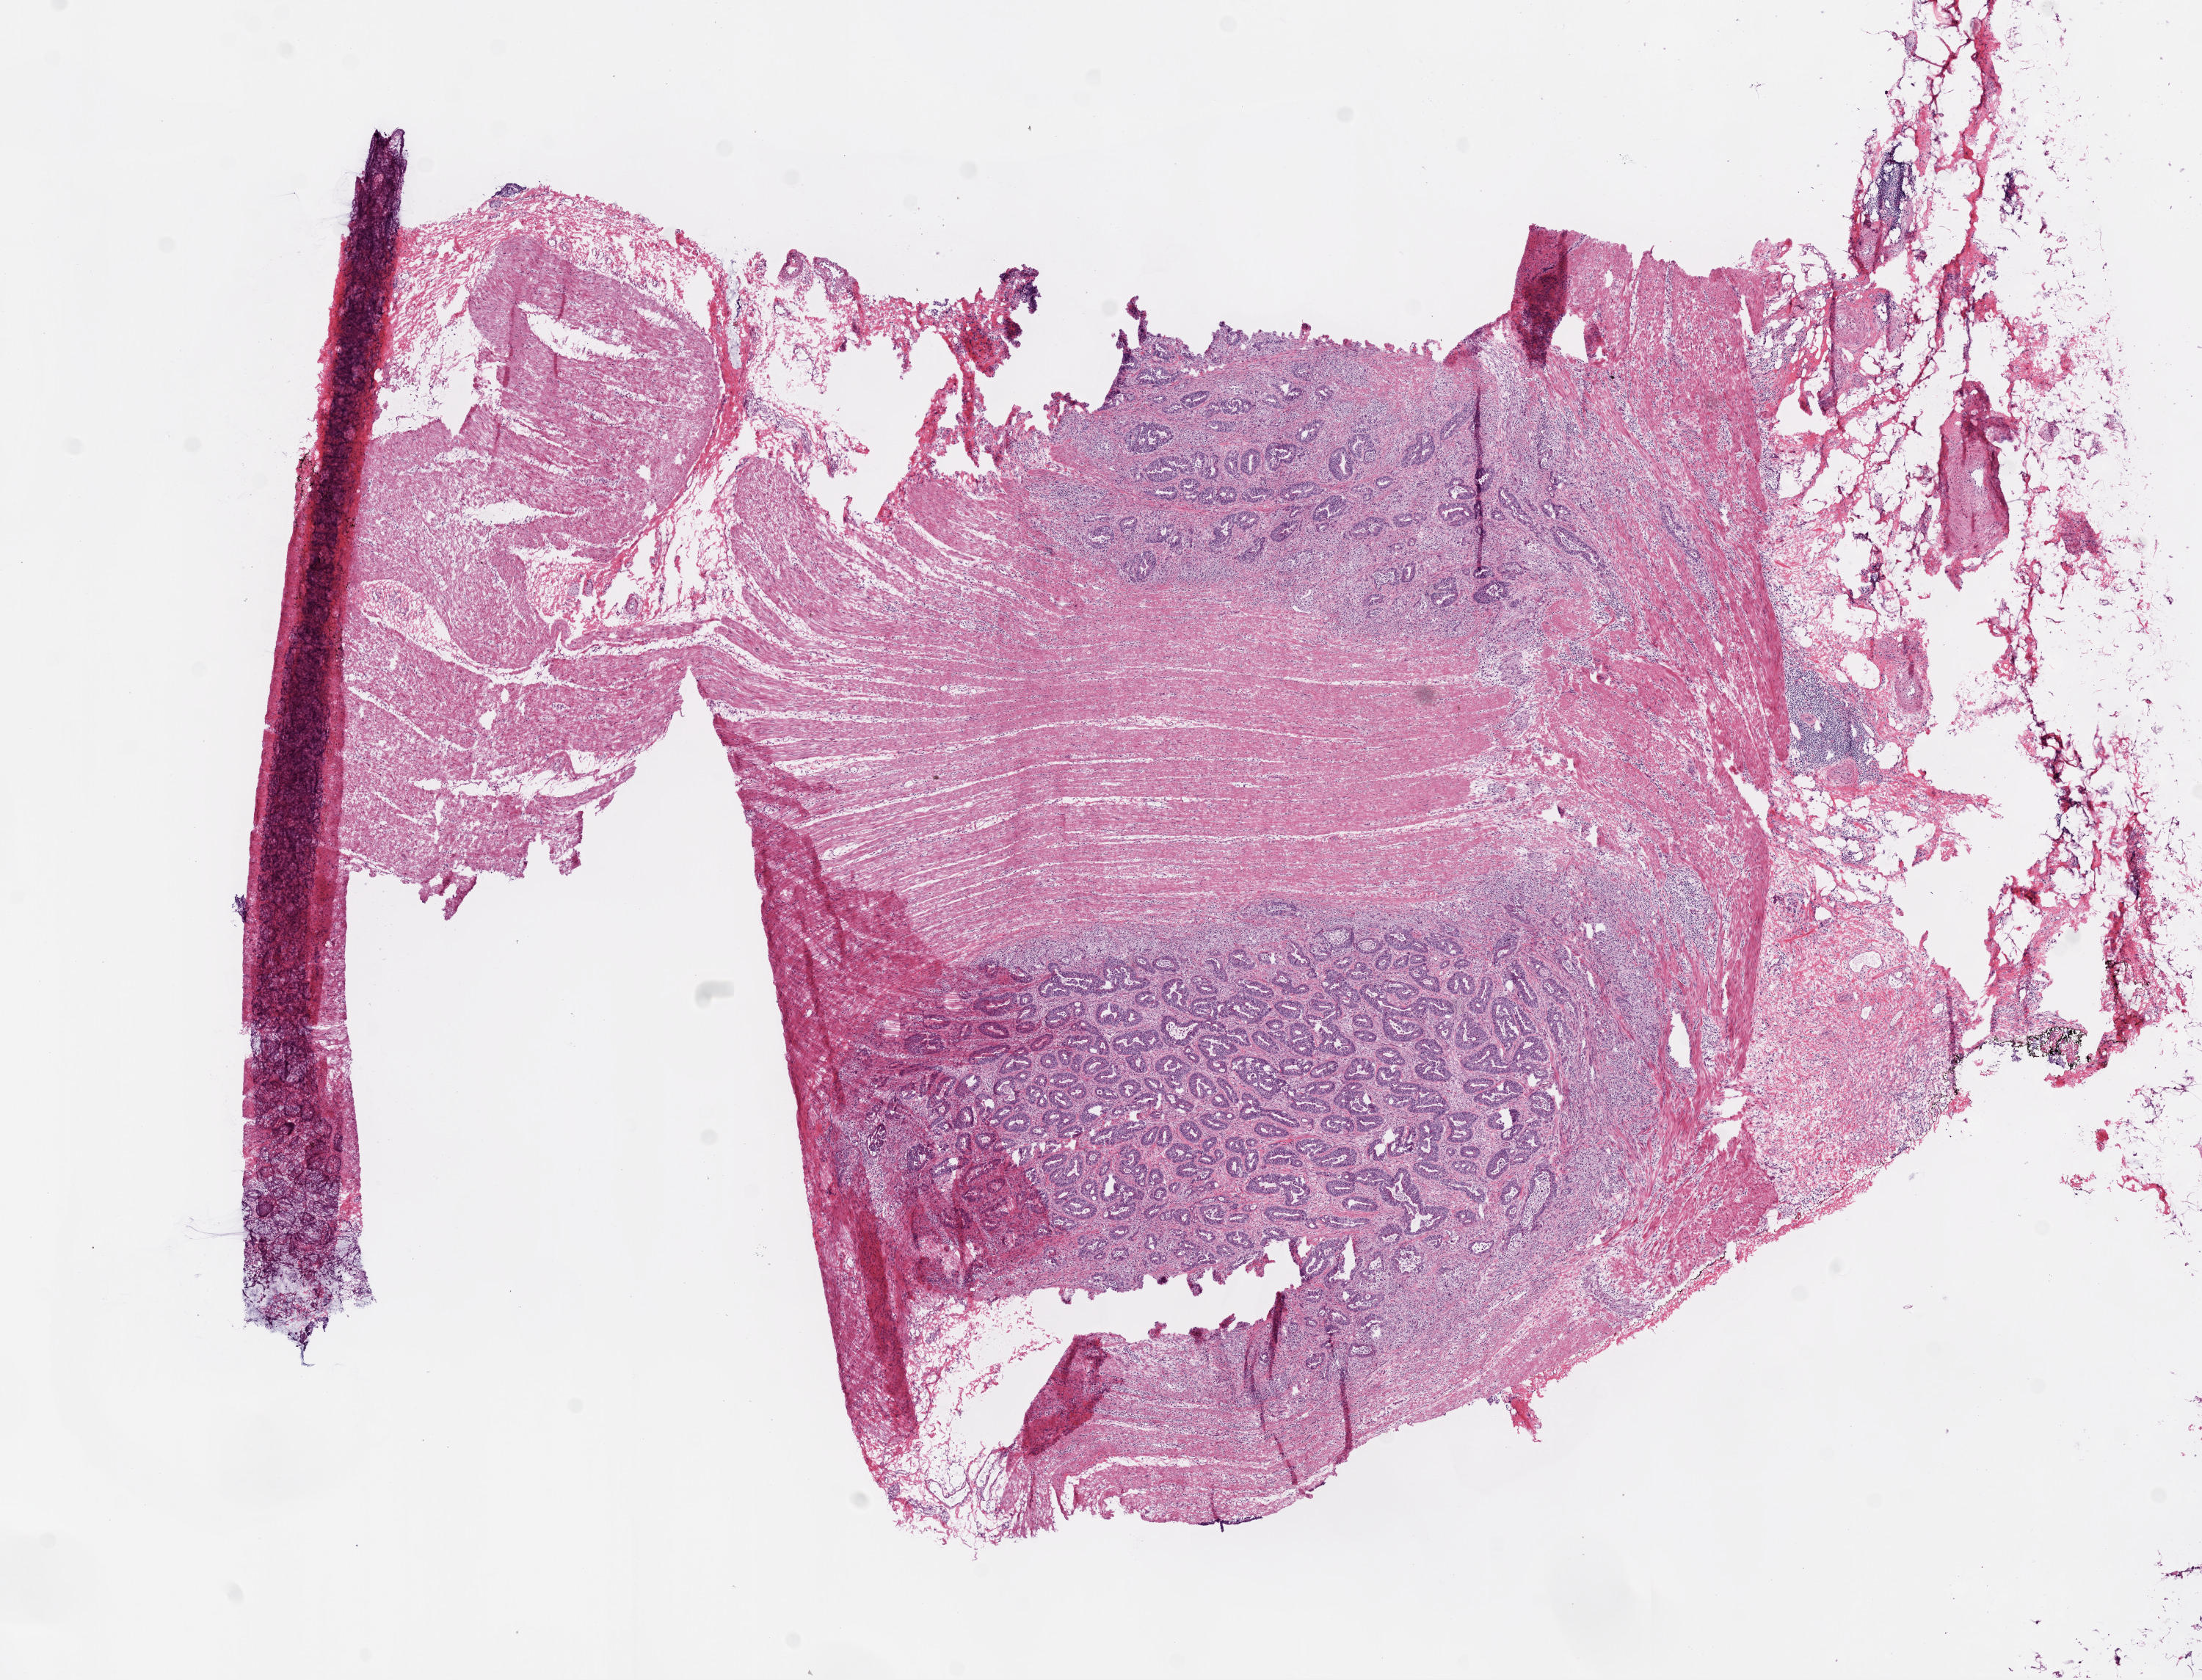
Whole-slide histology image, H&E, a low-resolution overview of the entire scanned area, about 12.0 x 9.2 mm; frozen section from the bottom of the tissue portion; primary tumour sample from the colon. Male, age 78 years at initial diagnosis. Slide review estimates, as recorded: tumour cells 50%, tumour nuclei 60%.
Pathologic diagnosis: Adenocarcinoma, NOS (sigmoid colon).